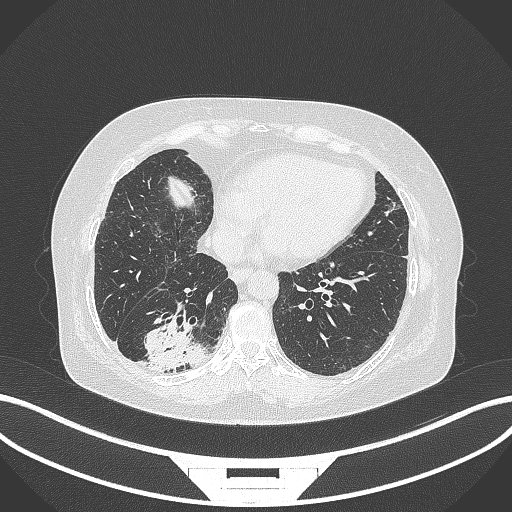
Chest CT, one axial slice; slice 71 of 296 in the series (ordered by position); 120 kVp; lung window (W 1500 / L -600 HU); 1 mm slice thickness; 512 × 512 image matrix. Patient: female, 65 years. Case-level facts recorded for this patient, not image findings: clinical TNM (as recorded): T2b N1 M0; histopathological grade: G1.
Structures marked on this image (bounding box drawn by a radiologist):
- lung tumour (recorded histology: adenocarcinoma): bounding box [x1, y1, x2, y2] px = [139, 320, 210, 373]